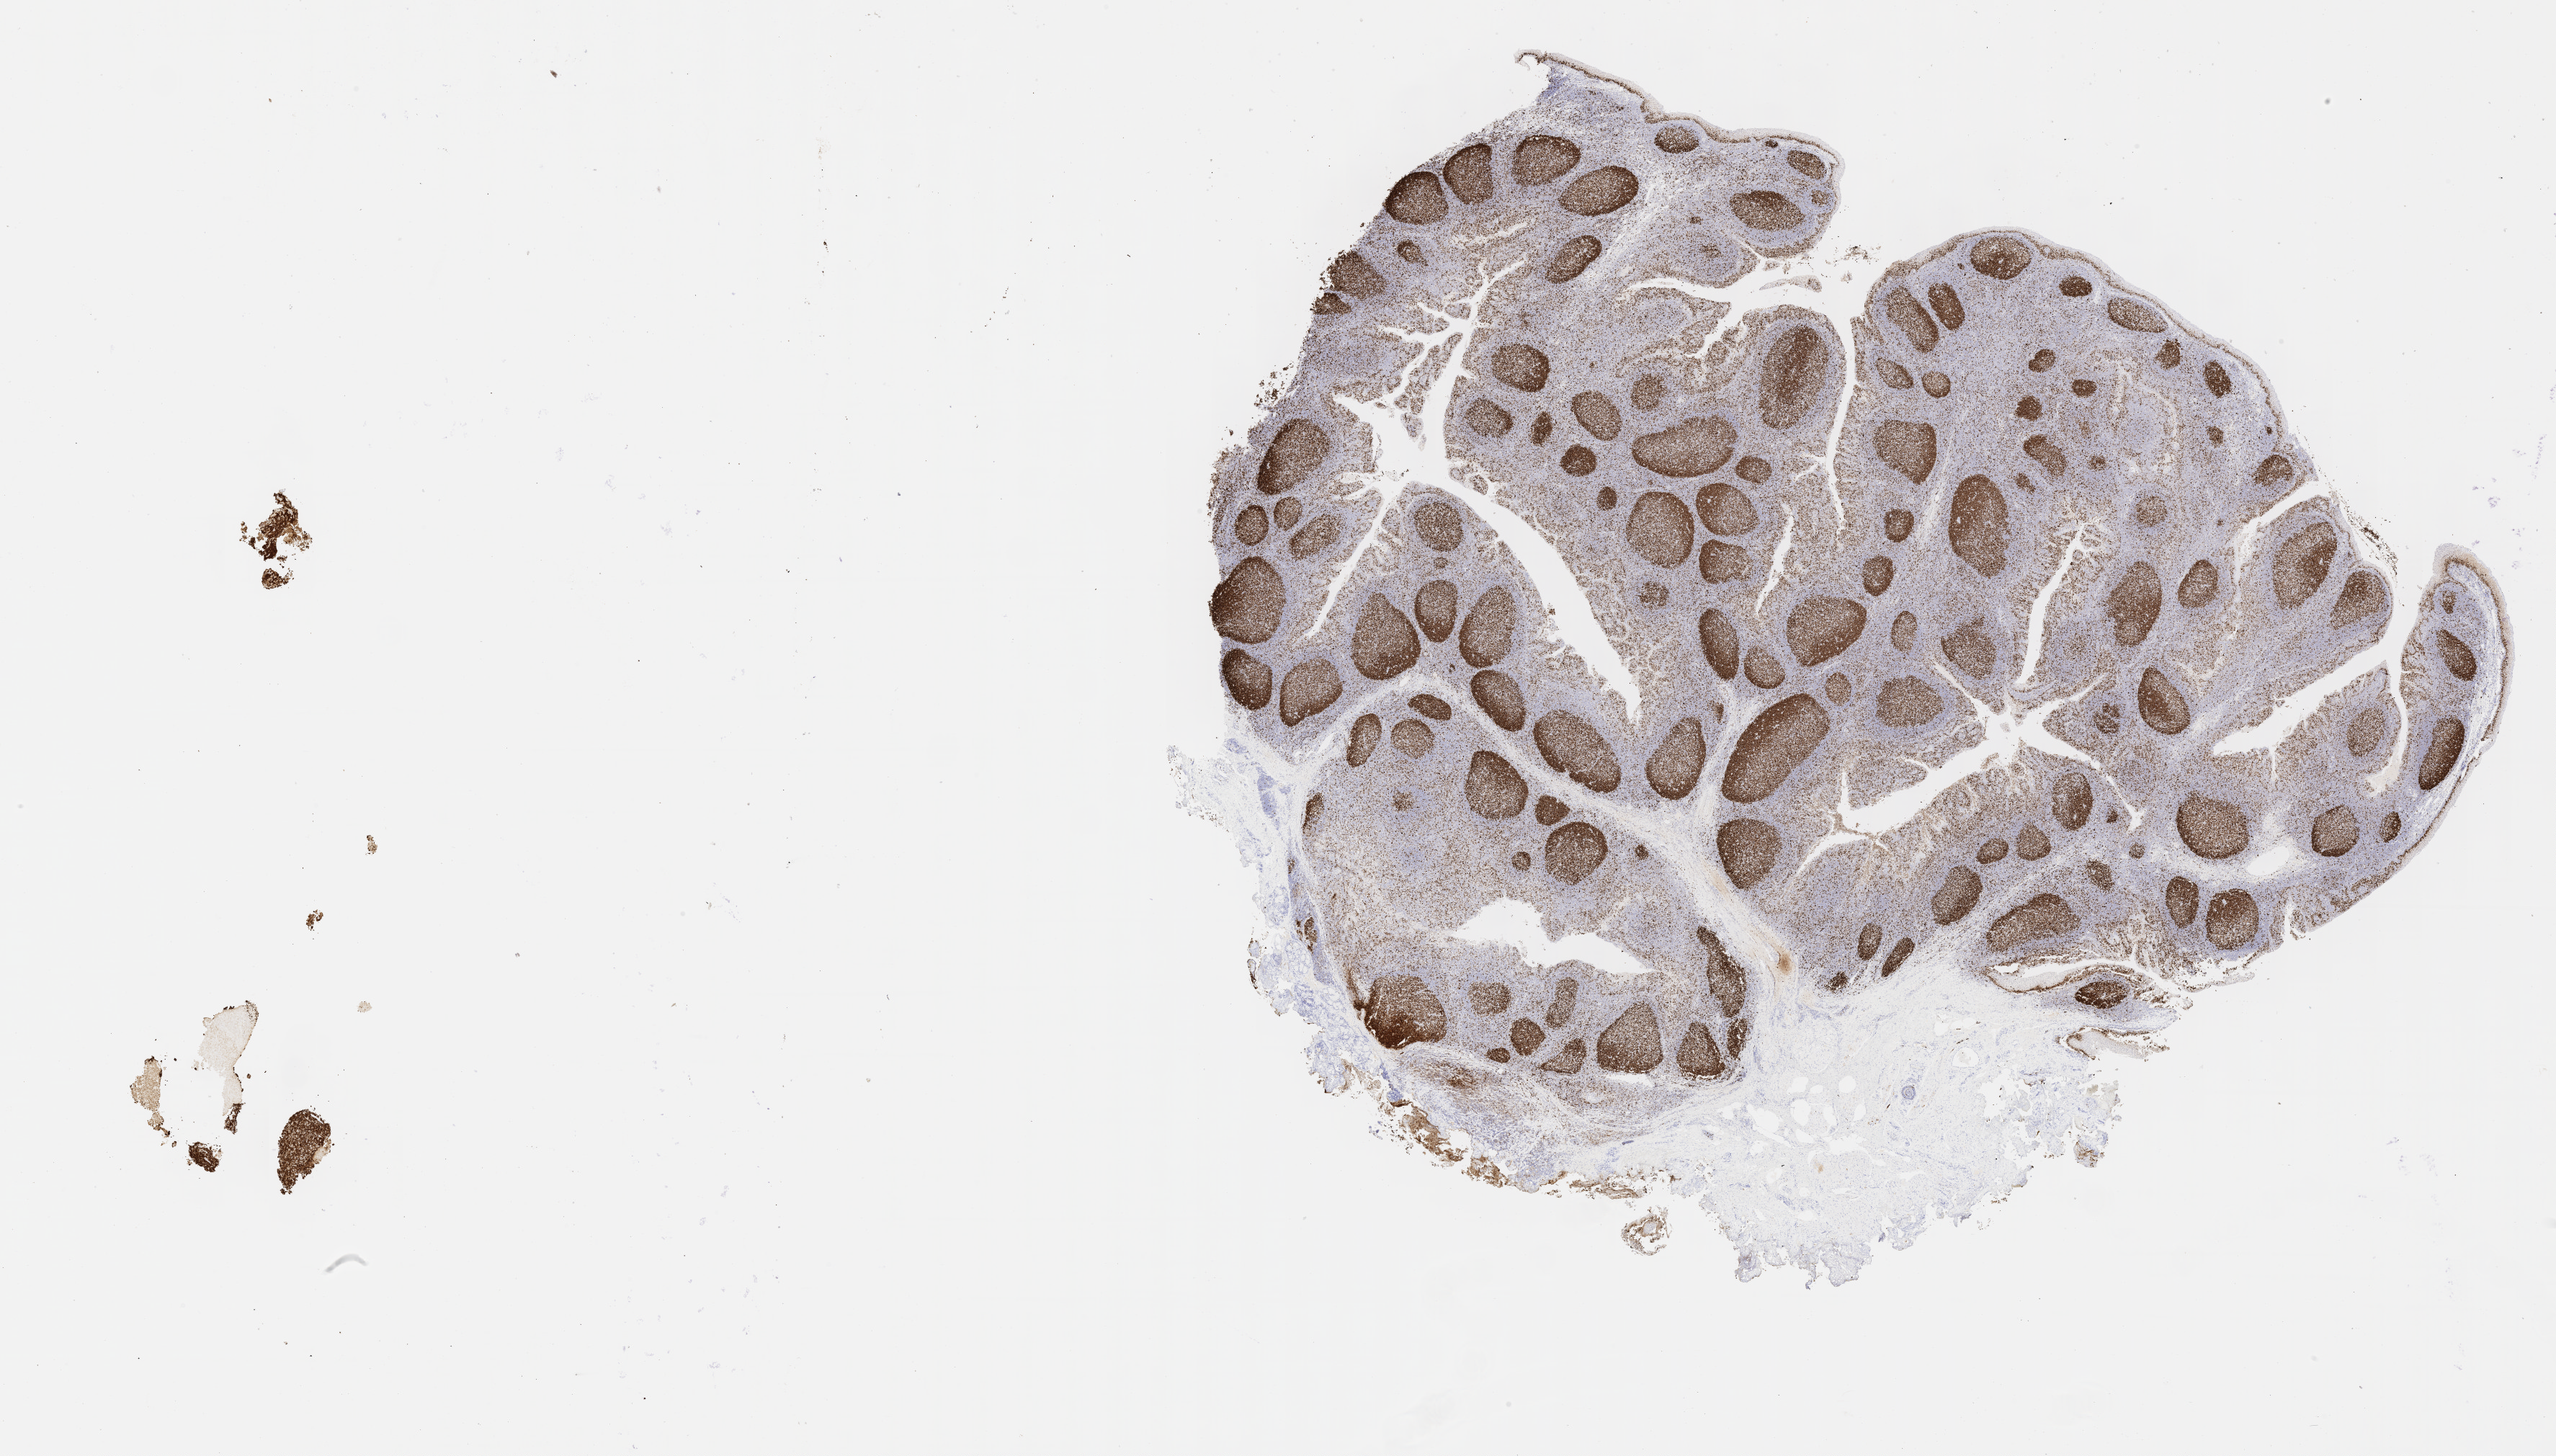
Whole-slide image, immunohistochemical stain for Ki-67 — whole scanned area (about 28.7 x 16.3 mm) shown as a low-resolution overview; specimen: tumor tissue; site: abdominal lymph node. Male, age 5 years at initial diagnosis.
Diagnosis: Diffuse large B-cell lymphoma, NOS.